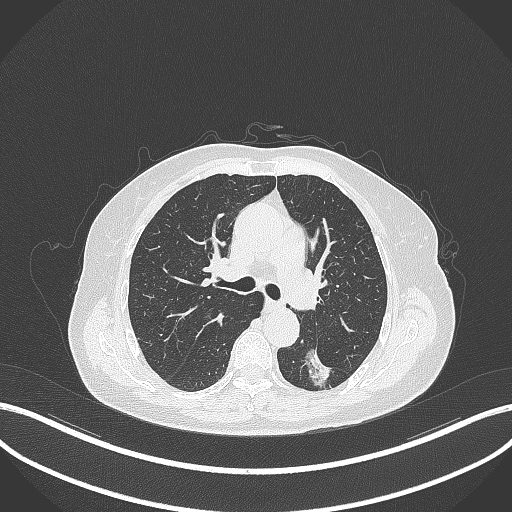
Chest CT, one axial slice. Slice 190 of 352 in the series (ordered by position). Lung window (W 1500 / L -600 HU). 1 mm slice thickness. 512 × 512 image matrix, field of view 400 × 400 mm. Female patient, age 70 years. From the clinical record (not read from this slice): clinical TNM (as recorded): T1c N0 M0.
Outlined on this slice (bounding box drawn by a radiologist):
- lung tumour (recorded histology: adenocarcinoma): bounding box [x1, y1, x2, y2] px = [298, 340, 338, 395]